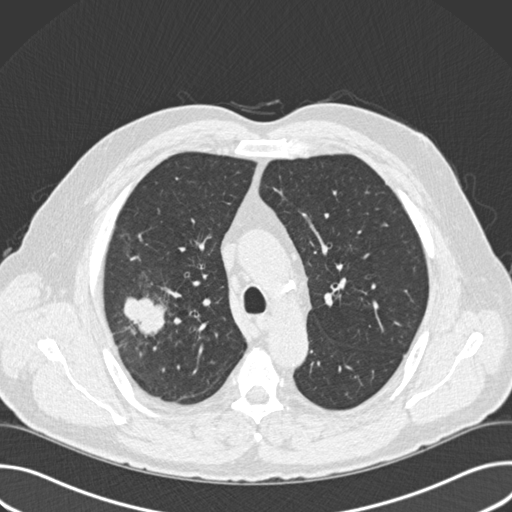
Low-dose screening chest CT, one axial slice. Slice 114 of 157 in the series (ordered by position). 120 kVp. Lung window (W 1500 / L -600 HU). 2 mm slice thickness. 512 × 512 image matrix, field of view 380 × 380 mm.
Outlined on this slice (expert manual segmentation):
- lesion 1 (tumor, upper lobe of right lung): bounding box <124,297,166,336> (left, top, right, bottom; pixels)